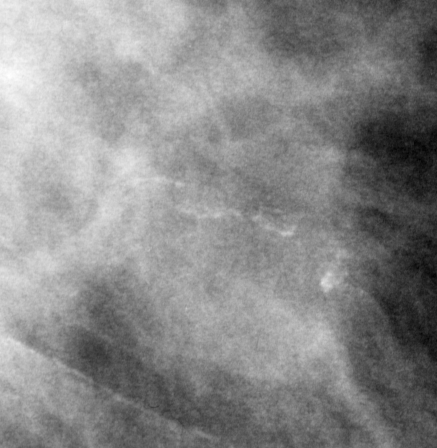
Cropped region of a digitized screen-film mammogram centred on a radiologist-marked abnormality, right breast, MLO view.
Finding: mass, shape irregular, margins spiculated; BI-RADS assessment category 5; subtlety rating 4 on a 1 (subtle) to 5 (obvious) scale; pathology (as recorded): malignant.